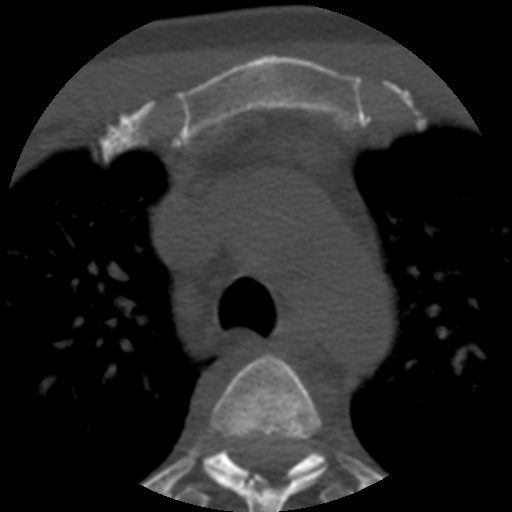
CT including the spine, one axial slice; slice 407 of 508 in the series (ordered by position); reconstruction kernel STANDARD; 120 kVp; bone window (W 1800 / L 400 HU); 1.25 mm slice thickness; 512 × 512 image matrix, field of view 160 × 160 mm. Patient age 57 years. Case-level facts recorded for this patient, not image findings: primary cancer: prostate.
Annotated regions visible in this slice (semi-automatic segmentation, software-assisted and operator-edited):
- T3 vertebra: bounding box (x1, y1, x2, y2) in pixels: (203, 355, 327, 512)
- T4 vertebra: (175, 436, 359, 505)